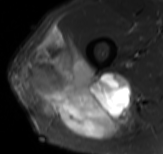
MRI of an extremity soft-tissue mass, one axial slice; slice 54 of 61 in the series (ordered by position); STIR; MR volume resampled by the dataset authors to the PET/CT grid (not the native acquisition matrix); 163 × 154 image matrix, field of view 159 × 150 mm. Male patient. Case-level facts recorded for this patient, not image findings: histological type: poorly differentiated synovial sarcoma; grade: high; site of the primary tumour: right buttock.
Annotated regions visible in this slice (expert contour drawn on MRI and transferred to this co-registered scan by the dataset authors):
- gross tumour volume including surrounding oedema: bounding box (x1, y1, x2, y2) in pixels: (23, 25, 143, 140)
- gross tumour volume (mass): (23, 25, 129, 140)